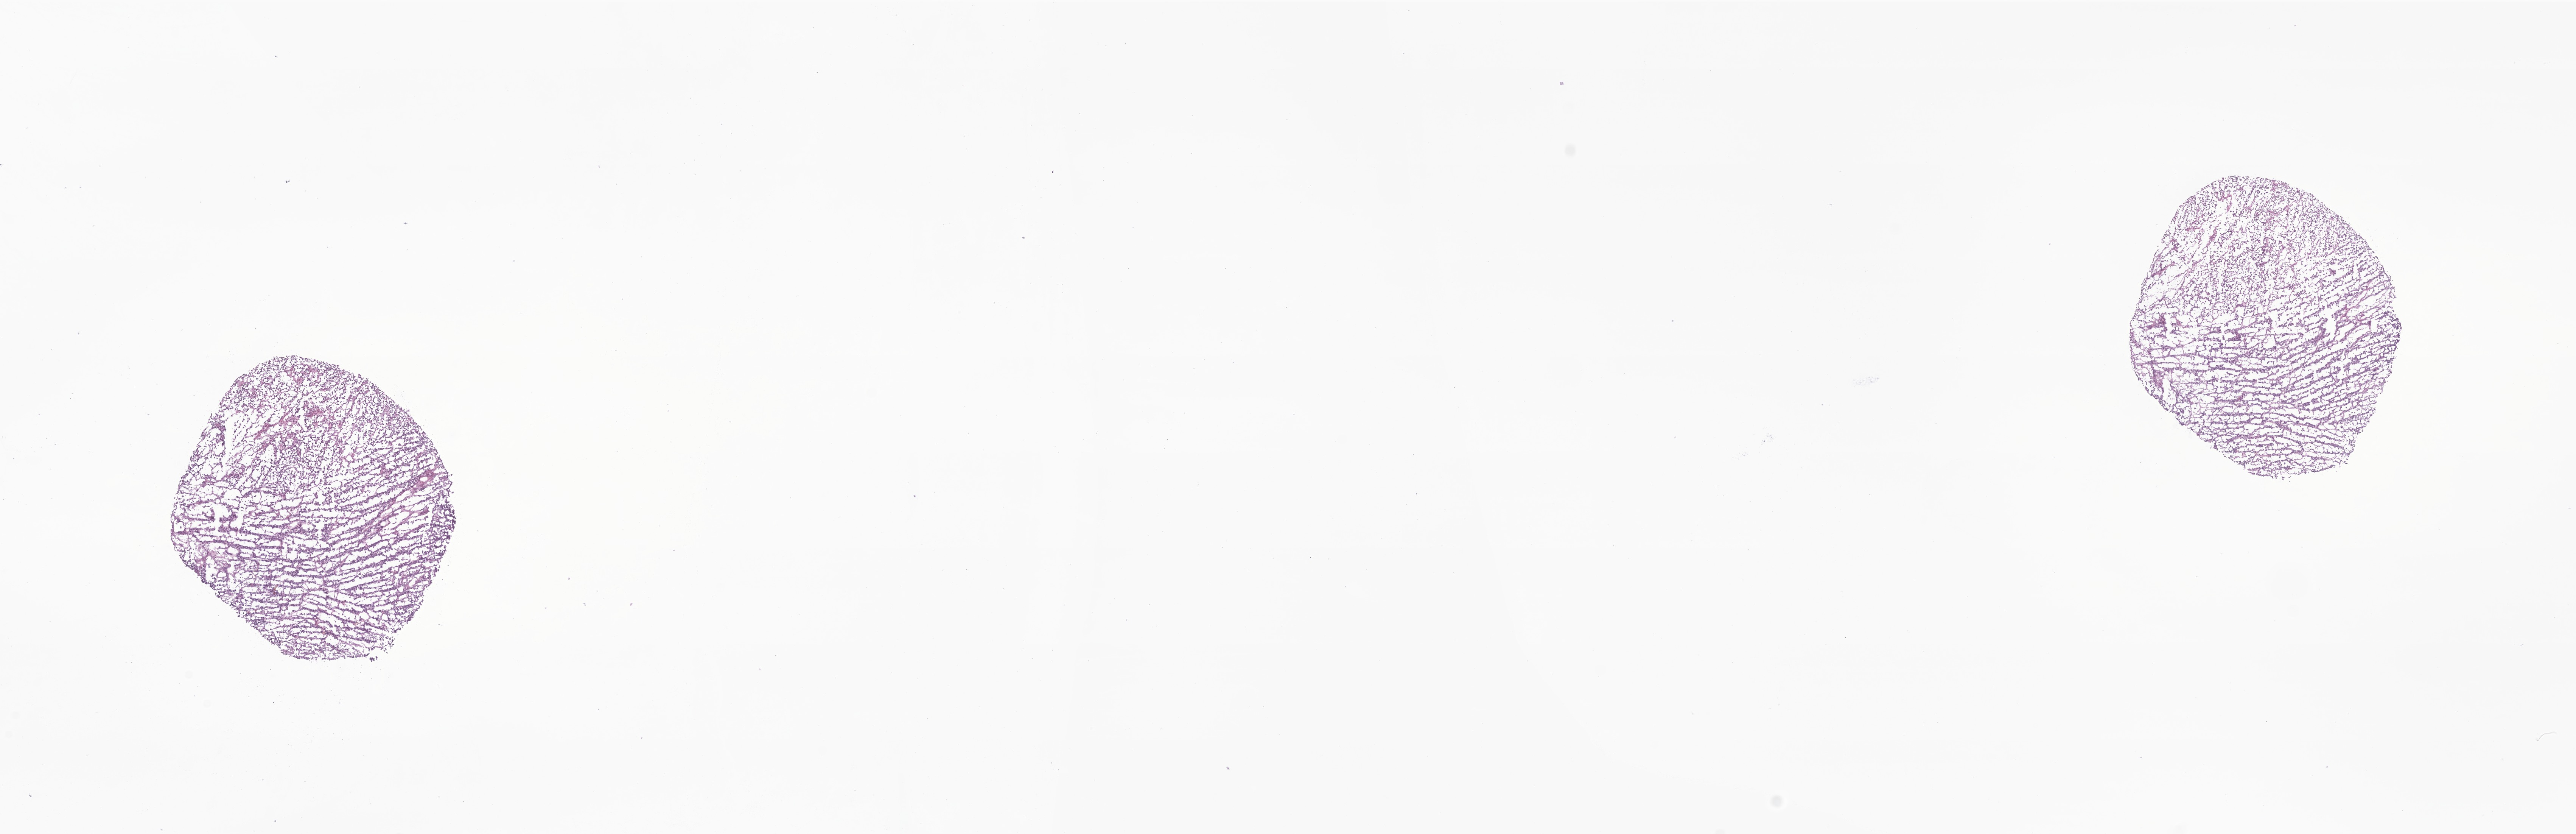
H&E whole-slide image of tumor tissue from the posterior mediastinum — shown as a low-resolution overview of the whole scanned area (about 28.7 x 9.3 mm). Frozen section. Patient: male, age 115 days.
Diagnosis: Neuroblastoma, NOS.